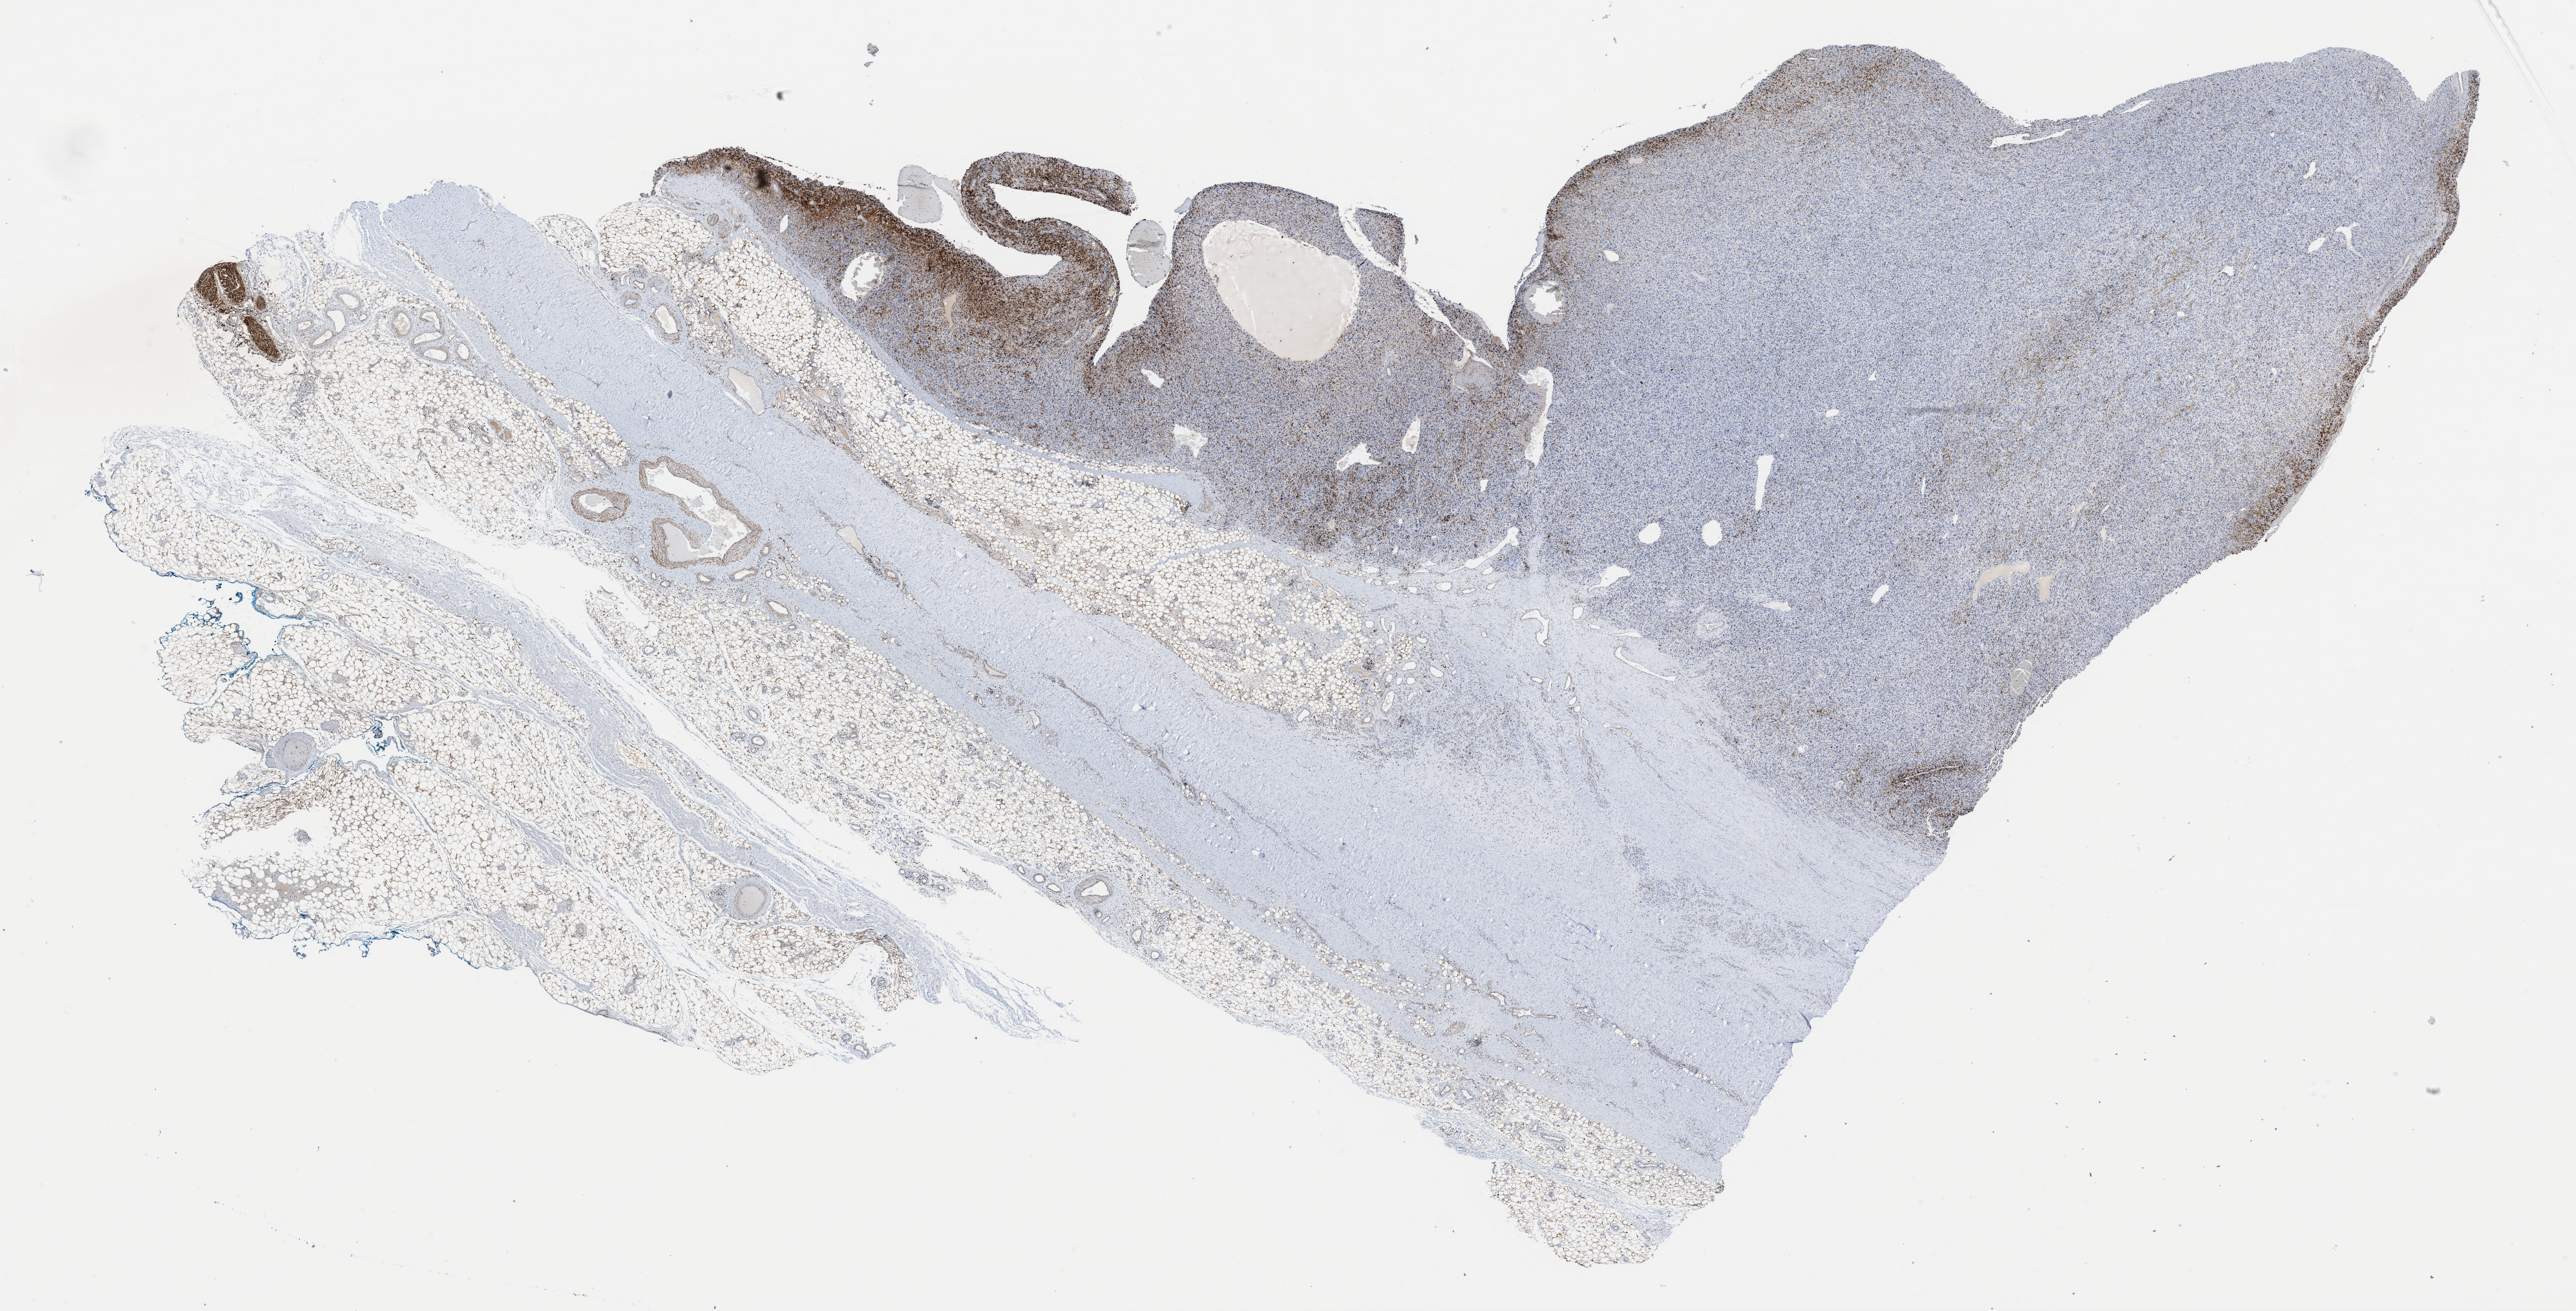
H&E-stained whole-slide image — whole scanned area (about 31.5 x 16.0 mm) shown as a low-resolution overview; formalin-fixed paraffin-embedded (FFPE) diagnostic section; sample: primary tumour, connective, subcutaneous and other soft tissues. Patient: female, age at initial diagnosis 75 years.
Diagnosis: Malignant fibrous histiocytoma (connective, subcutaneous and other soft tissues of lower limb and hip).